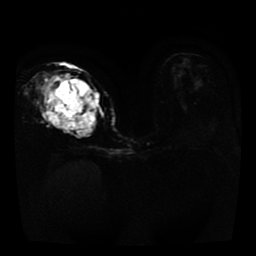
Breast MRI, one axial slice; position 20 of 41 along the scan axis; diffusion-weighted series; image 2 of 4 stored at this slice position (different b-values; order by instance number); 1.5 T; 256 × 256 image matrix, field of view 330 × 330 mm. Female patient.
Outlined on this slice (manually delineated by an expert):
- tumour on diffusion-weighted imaging: bounding box <42,74,99,135> (left, top, right, bottom; pixels)